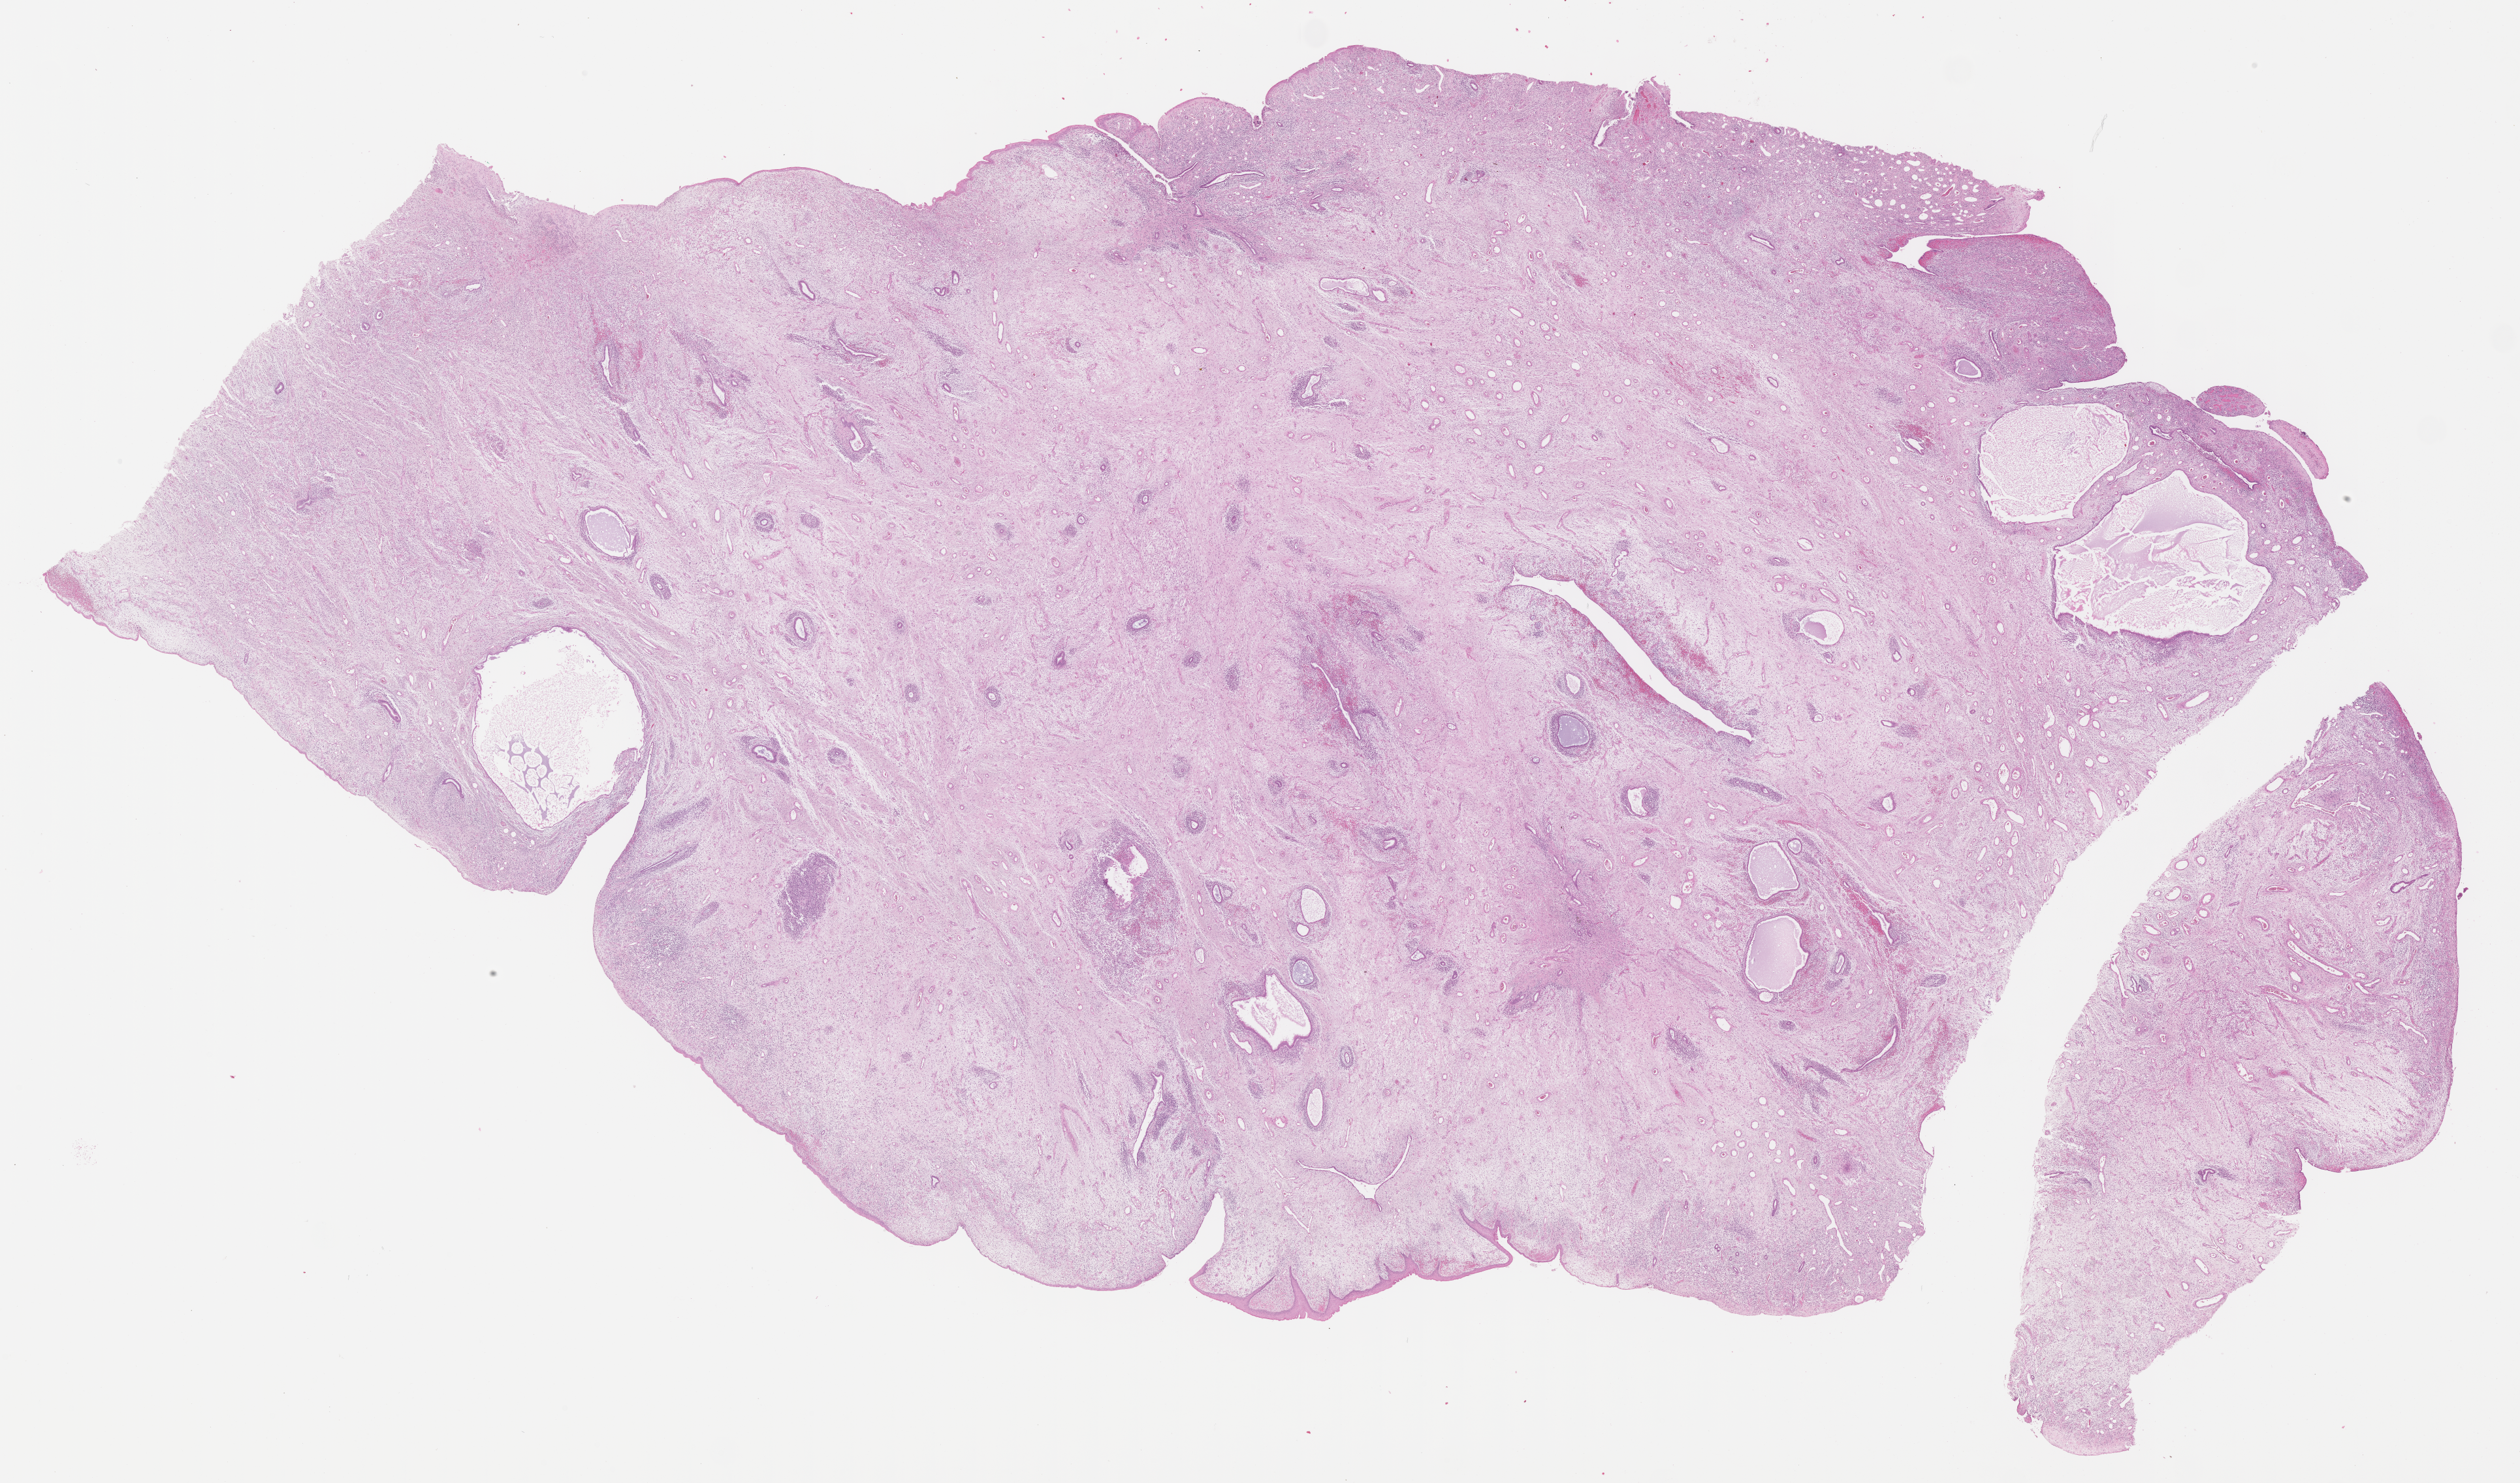
Digitized haematoxylin and eosin-stained section of tumor tissue — a low-resolution overview of the entire scanned area, about 31.2 x 18.4 mm, formalin-fixed, paraffin-embedded (FFPE) tissue, site: uterus. Female patient, age at diagnosis 15.7 years.
* metastatic status at presentation (as recorded): non-metastatic (confirmed)
* diagnosis: rhabdomyosarcoma; histological classification: embryonal rhabdomyosarcoma
* stage (as recorded): 1